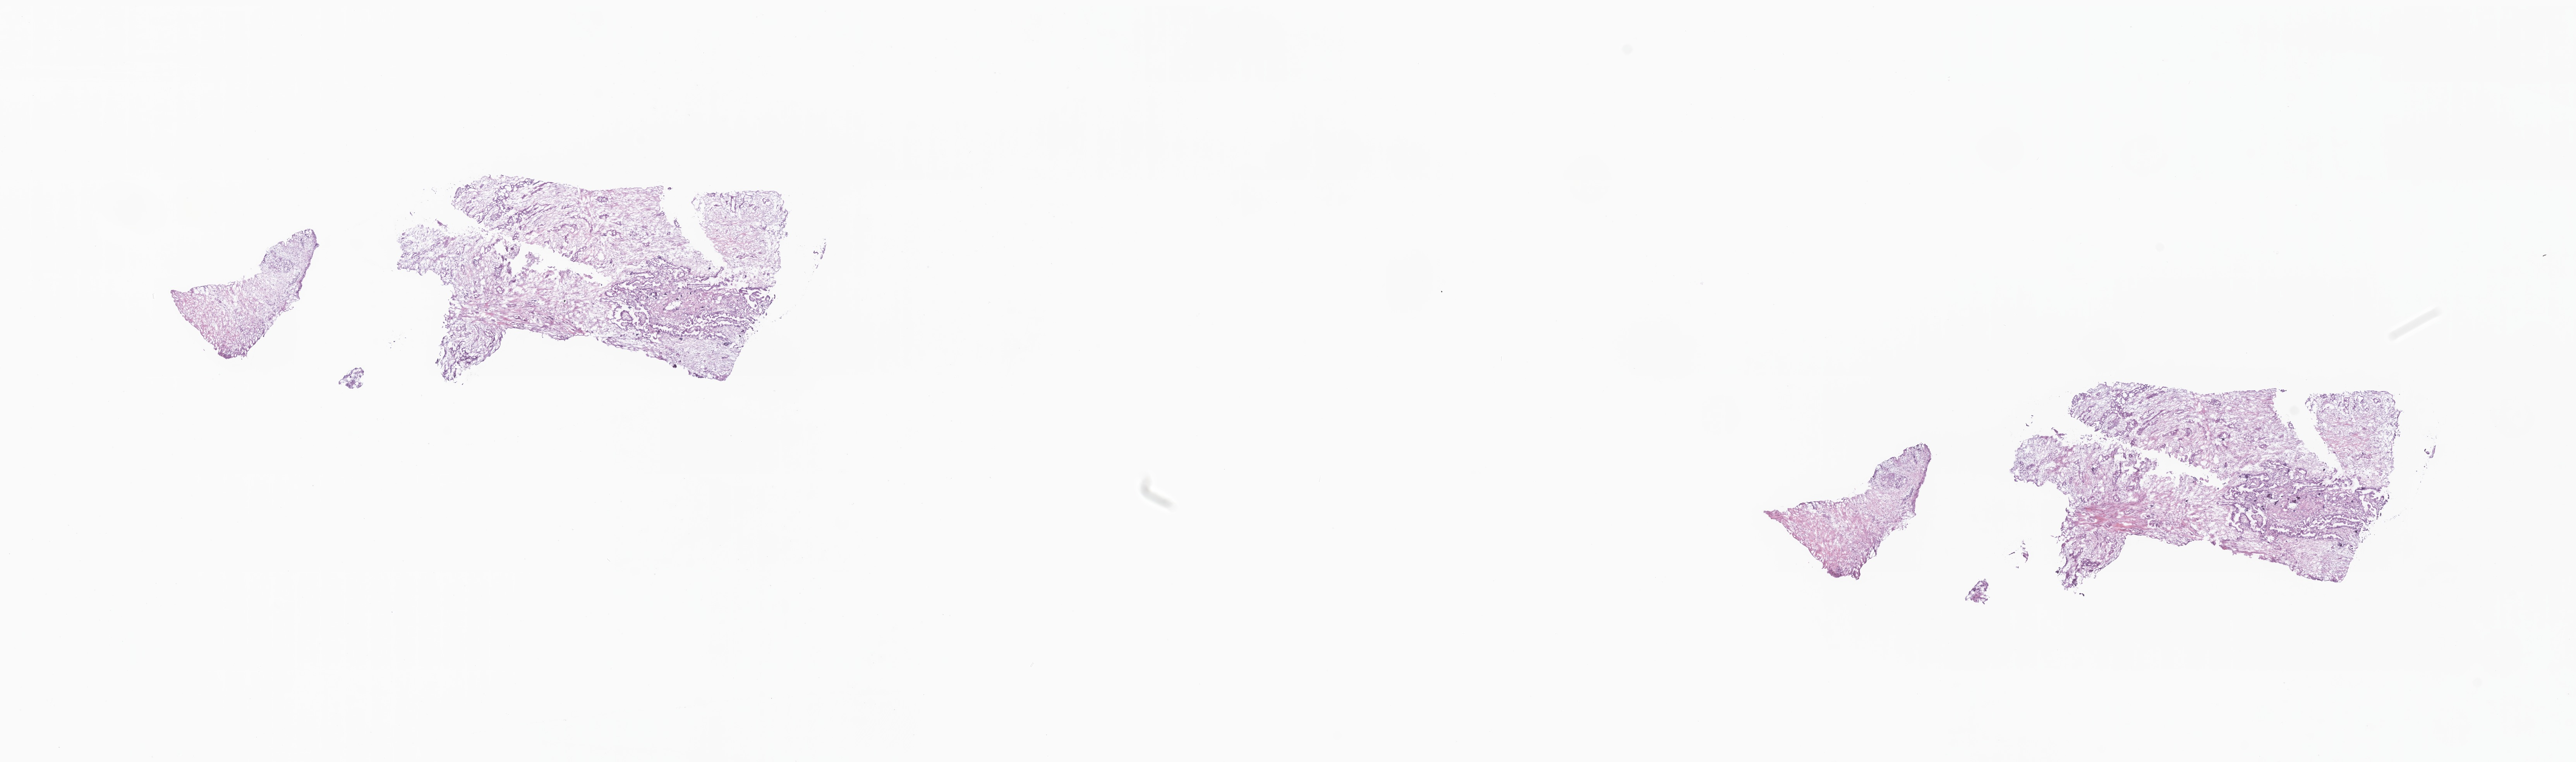
Digitized haematoxylin and eosin-stained section — a low-resolution overview of the entire scanned area, about 28.0 x 8.3 mm; frozen section (tissue freezing medium); specimen: primary tumor; site: tail of pancreas. Patient: male, age at initial diagnosis 69 years. Pathologist review of this section (percent, as recorded): tumor cells 30%, tumor nuclei 40%, stromal cells 70%, necrosis 0%, normal cells 0%. Infiltration values recorded for this section: lymphocyte infiltration 0%, monocyte infiltration 0%, neutrophil infiltration 0%.
• diagnosis: Infiltrating duct carcinoma, NOS
• section: bottom of the tissue portion